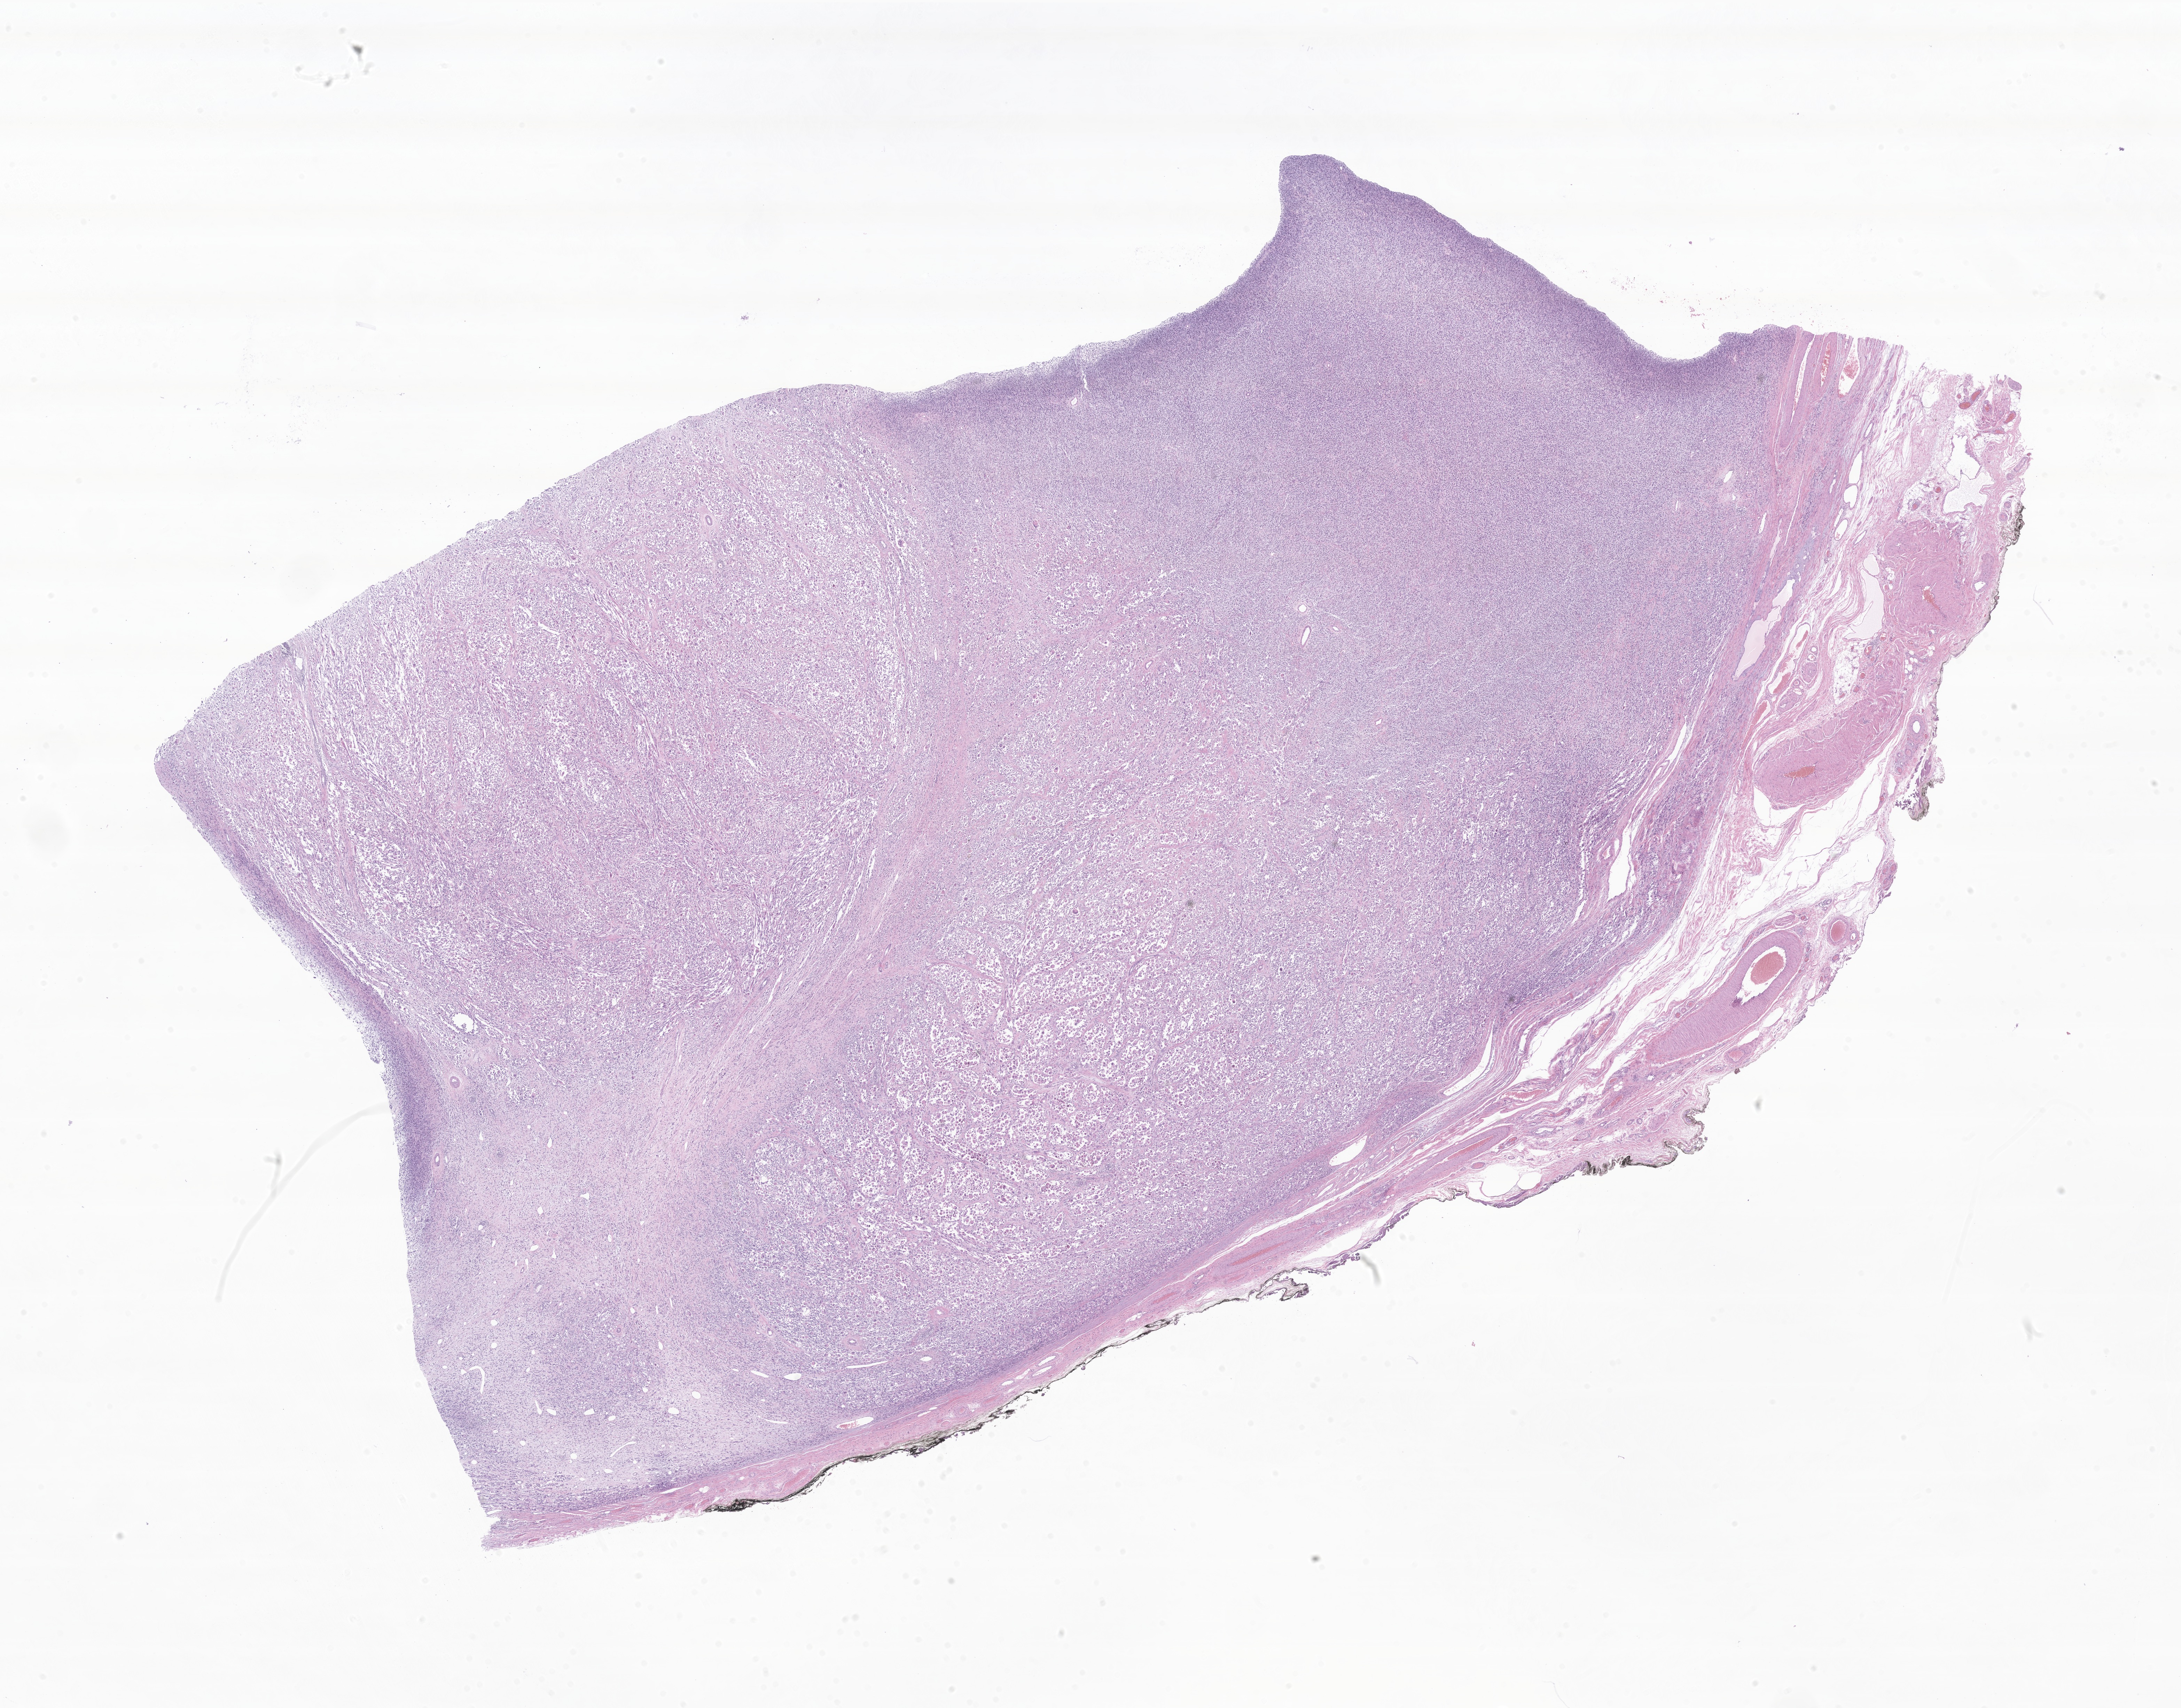
Digitized hematoxylin and eosin (H&E)-stained section of tumor tissue from the testis, whole scanned area (about 26.4 x 20.7 mm) shown as a low-resolution overview, formalin-fixed, paraffin-embedded (FFPE) tissue. Male patient, age 253 months (21 years 1 month).
Diagnosis (ICD-O-3 morphology term): Embryonal rhabdomyosarcoma, NOS.